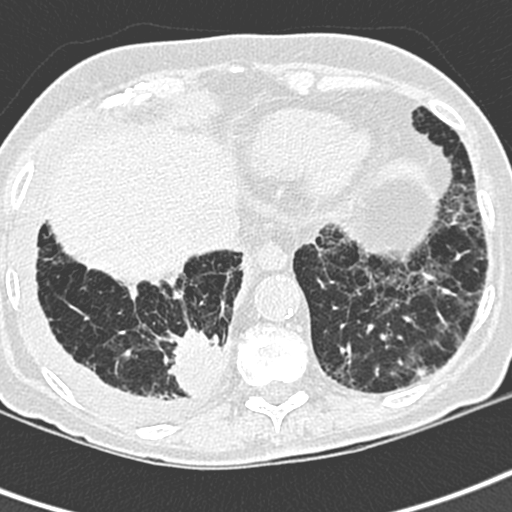
Low-dose screening chest CT, one axial slice. Slice 70 of 220 in the series (ordered by position). Lung window (W 1500 / L -600 HU). 1.3 mm slice thickness. 512 × 512 image matrix, field of view 288 × 288 mm.
Annotated regions visible in this slice (manually delineated by an expert):
- lesion 1 (tumor, lower lobe of right lung): bounding box <166,326,223,396> (left, top, right, bottom; pixels)
- lesion 2 (nodule, lower lobe of left lung): <417,367,426,376>